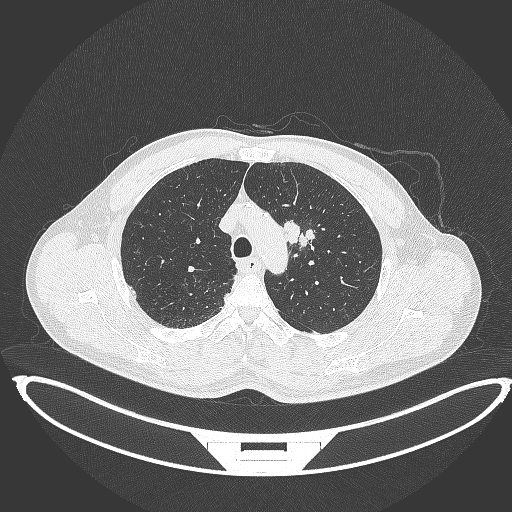
Chest CT, one axial slice. Slice 333 of 395 in the series (ordered by position). Lung window (W 1500 / L -600 HU). 1 mm slice thickness. 512 × 512 image matrix. Male patient, age 60 years. Case-level facts recorded for this patient, not image findings: clinical TNM (as recorded): T2a N0 M0; histopathological grade: G1-G2.
Annotated regions visible in this slice (bounding box drawn by a radiologist):
- lung tumour (recorded histology: squamous cell carcinoma): box from (x=281, y=219) to (x=314, y=251) px